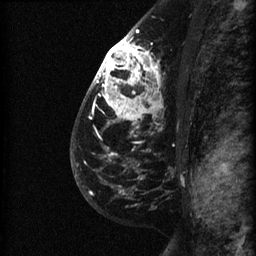
Breast MRI (dynamic contrast-enhanced), one sagittal slice. Position 43 of 60 along the scan axis. Dynamic contrast-enhanced series, image 2 of 3 at this slice position (ordered by acquisition). 1.5 T. TE 4.2 ms, TR 22.7 ms. 1.5 mm slice thickness. 256 × 256 image matrix, field of view 180 × 180 mm. Female patient, age 48 years. From the clinical record (not read from this slice): setting: breast cancer imaged before/during neoadjuvant chemotherapy; receptor status: triple-negative.
Outlined on this slice (semi-automatically segmented with operator editing):
- analysis volume of interest (the breast-tissue region the enhancement analysis was run in; not a lesion): box from (x=89, y=27) to (x=189, y=180) px
- tumour enhancement mask (voxels above the 90 % enhancement threshold inside the analysis volume of interest): (x=93, y=29)–(x=156, y=160)